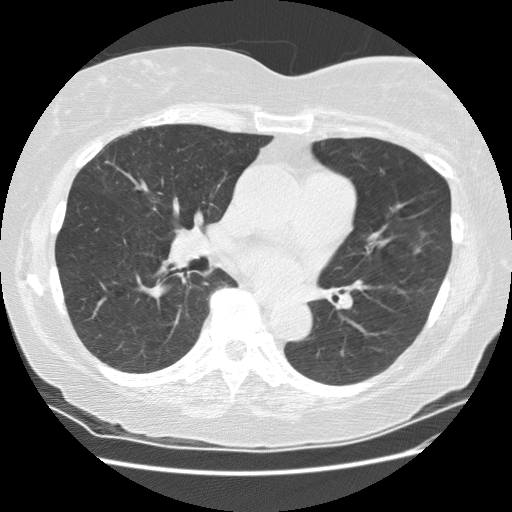
Low-dose screening chest CT, one axial slice. Slice 94 of 180 in the series (ordered by position). 120 kVp. Lung window (W 1500 / L -600 HU). 2.5 mm slice thickness. 512 × 512 image matrix.
Structures marked on this image (manually delineated by an expert):
- lesion 1 (tumor, upper lobe of left lung): bounding box <413,245,424,255> (left, top, right, bottom; pixels)